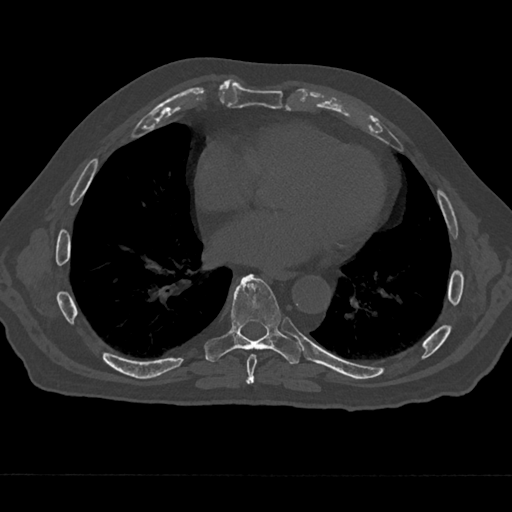
CT including the spine, one axial slice; slice 329 of 797 in the series (ordered by position); reconstruction kernel Br40s/3; 120 kVp; bone window (W 1800 / L 400 HU); 512 × 512 image matrix, field of view 377 × 377 mm. Patient: male, 75 years. Case-level facts recorded for this patient, not image findings: primary cancer: renal; vertebrae with lytic lesions (as recorded): T4.
Structures marked on this image (semi-automatic segmentation, software-assisted and operator-edited):
- T7 vertebra: bounding box (x1, y1, x2, y2) in pixels: (245, 354, 258, 384)
- T8 vertebra: (204, 274, 301, 384)